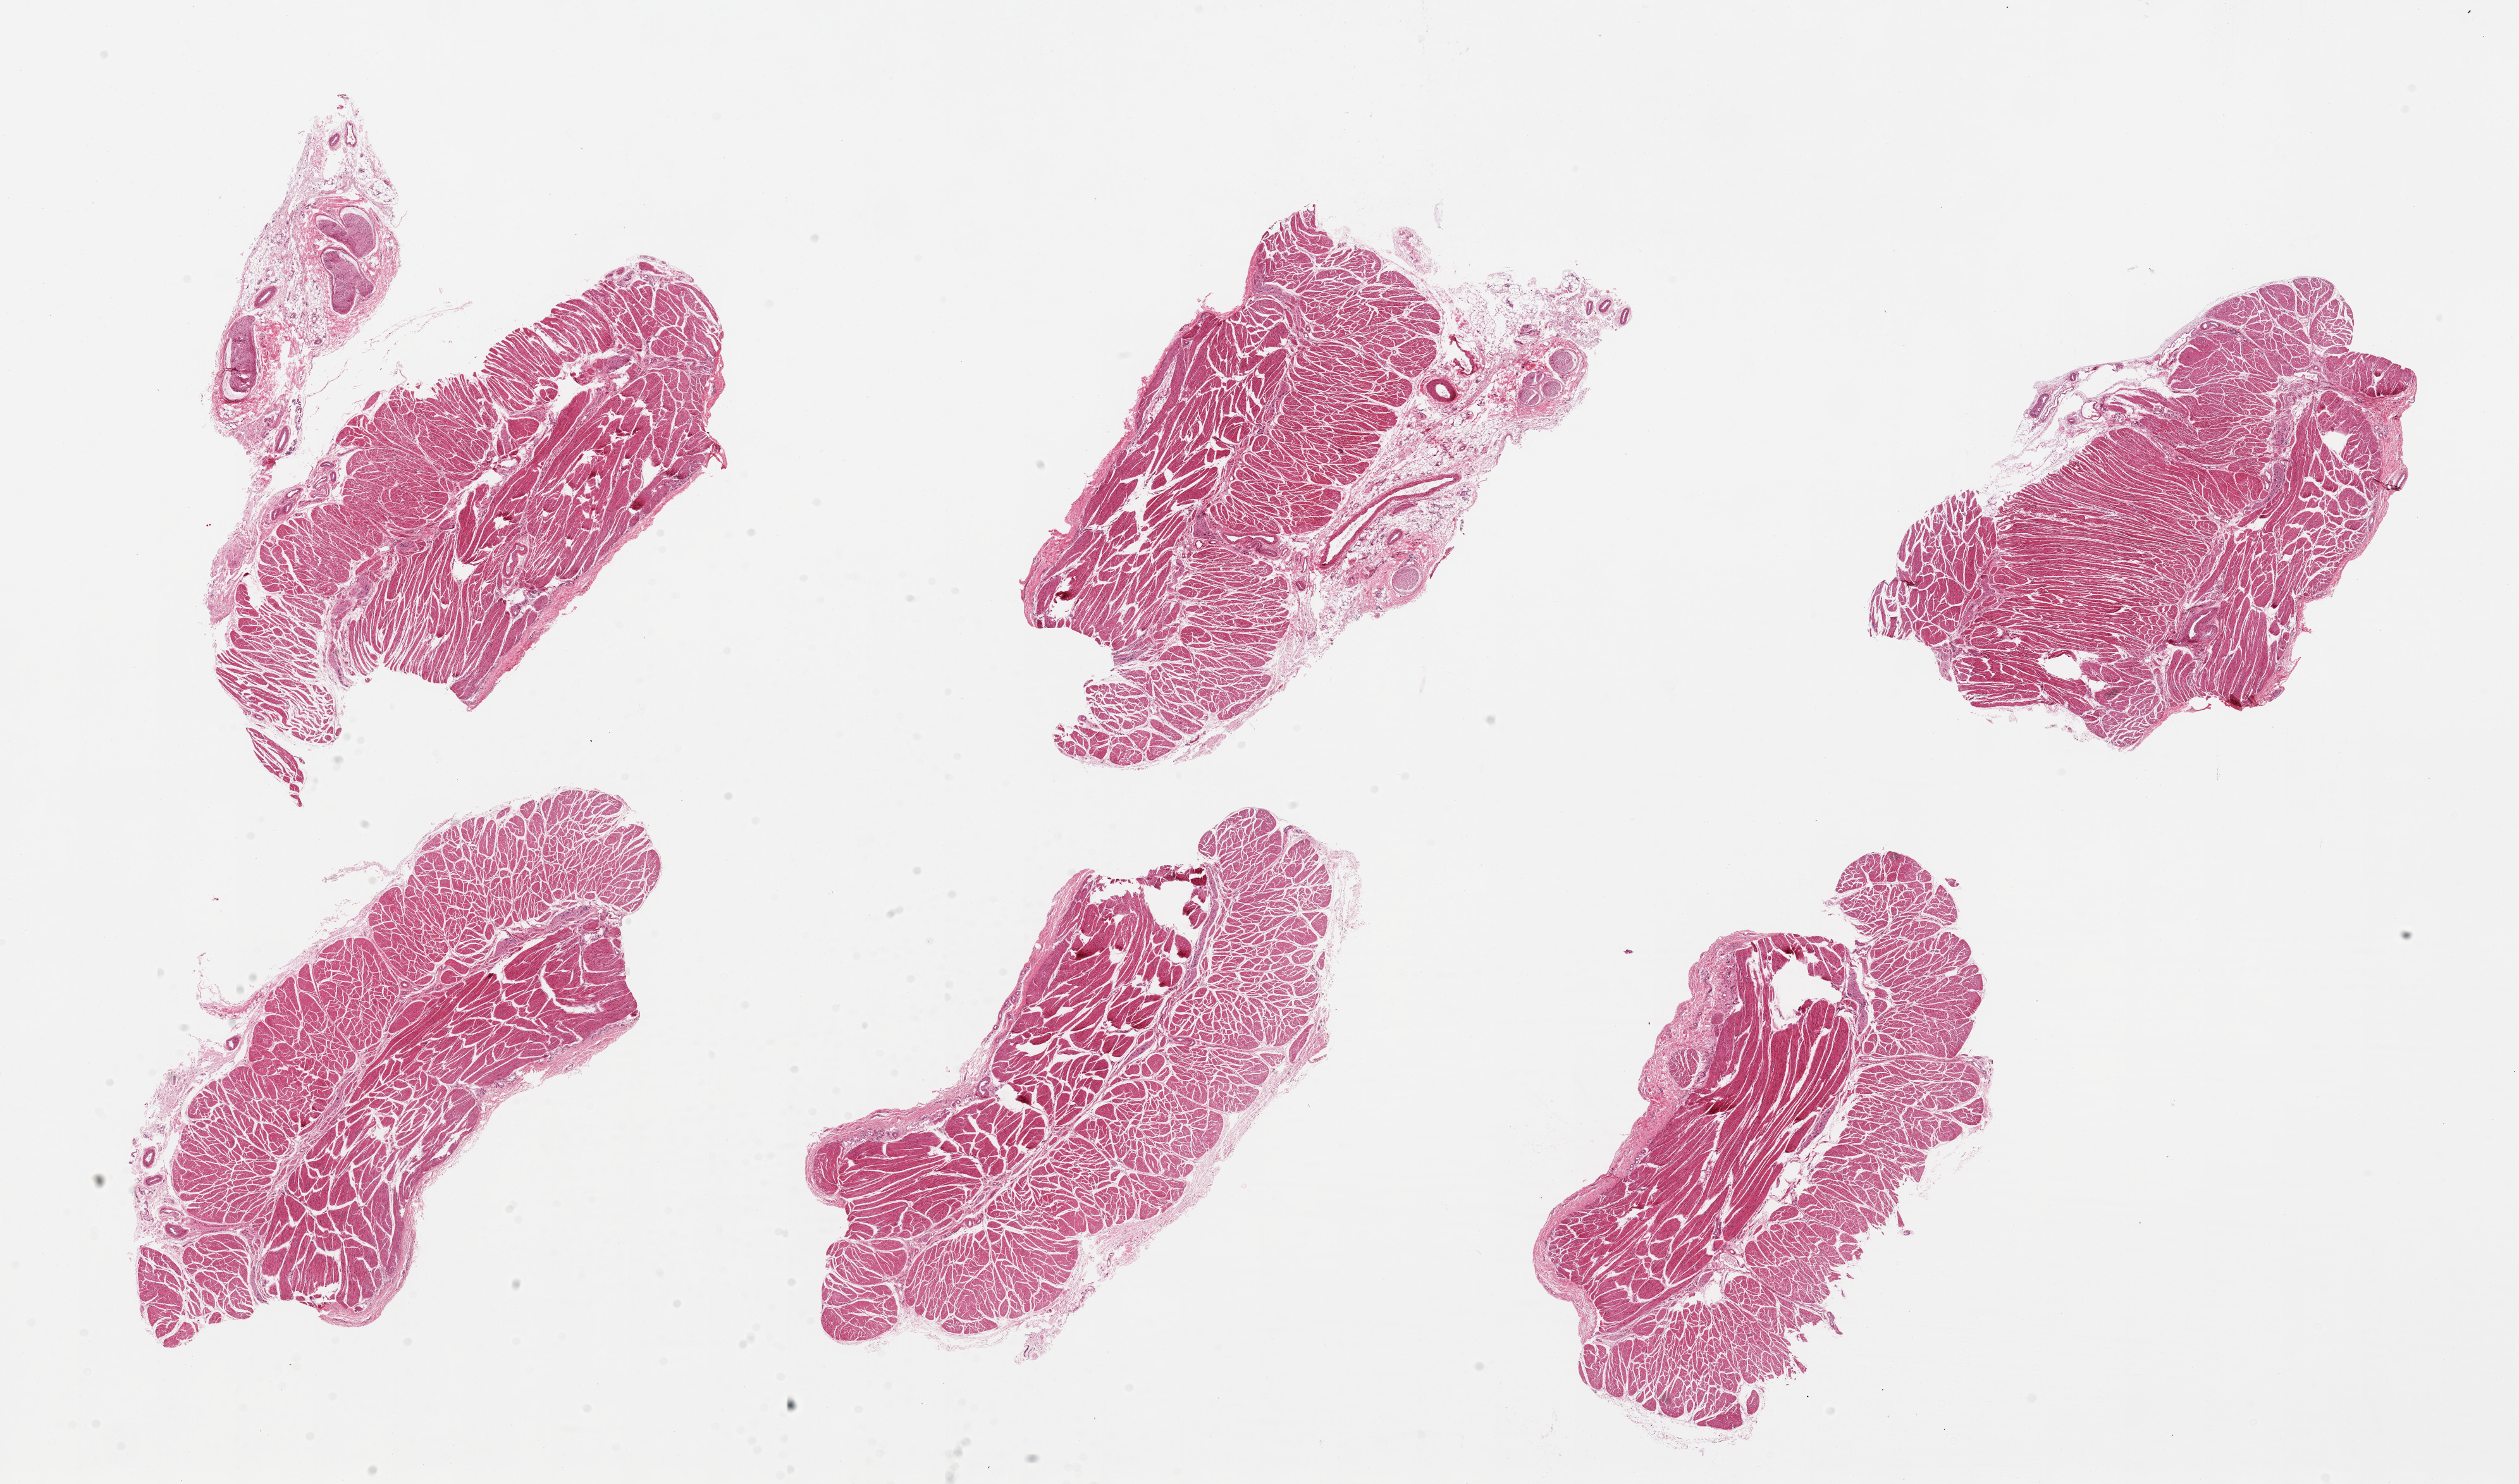
Haematoxylin and eosin whole-slide image, brightfield — low-resolution overview of the scanned area, about 31.5 x 18.6 mm (slide scanned at 20x). PAXgene-fixed paraffin-embedded (PFPE) section. Section of esophageal muscle (target tissue). Donor tissue sample. Donor sex: male.
Review note (as recorded): 6 pieces, up to 9x4mm; mainly muscularis, a few with adherent serosa containing vessels or peripheral nerve.